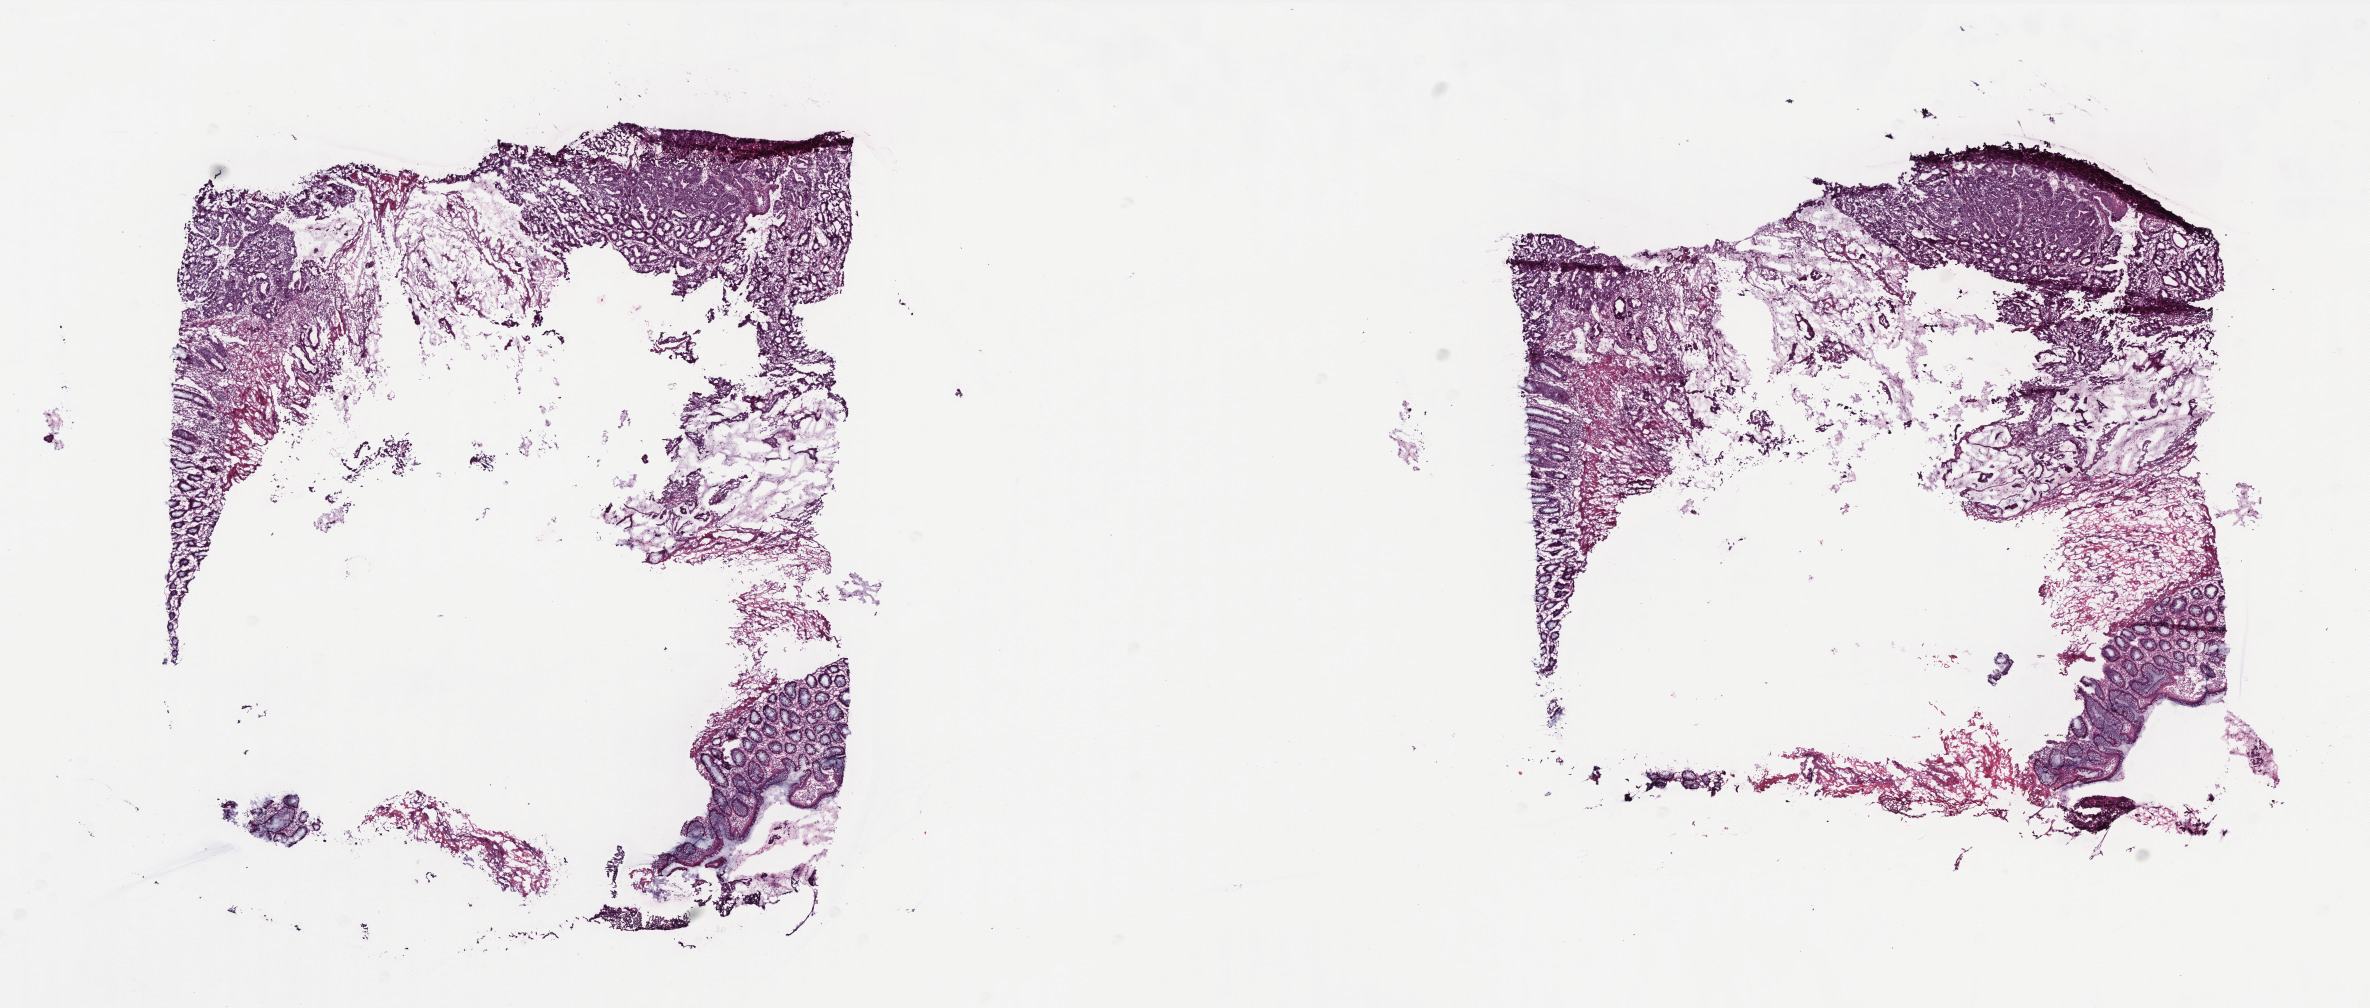
H&E-stained whole-slide image — a low-resolution overview of the entire scanned area, about 19.0 x 8.1 mm. Frozen section from the top of the tissue portion. Colon, primary tumour sample. Female, age 47 years at initial diagnosis. Pathologist review of this section (percent, as recorded): tumour cells 63%, tumour nuclei 80%, normal cells 30%, stromal cells 1%, necrosis 1%. Infiltration values recorded for this section: lymphocyte infiltration 10%, monocyte infiltration 2%, neutrophil infiltration 1%.
Pathologic diagnosis: Mucinous adenocarcinoma (rectosigmoid junction). AJCC pathologic stage: IIIC (6th edition).